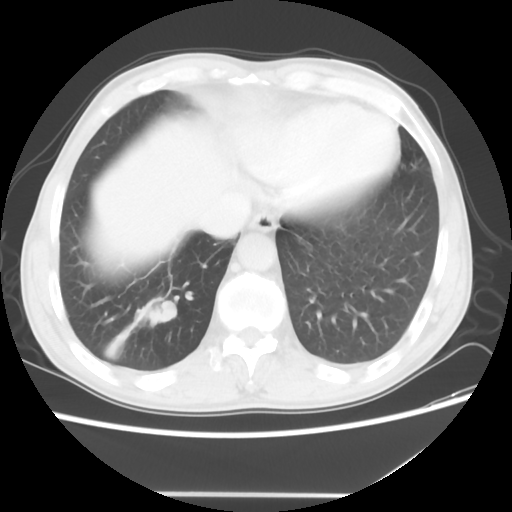
Chest CT, one axial slice; position 12 of 56 along the scan axis; 120 kVp; lung window (W 1500 / L -600 HU); 5 mm slice thickness; 512 × 512 image matrix, field of view 344 × 344 mm. Male patient, age 65 years. From the clinical record (not read from this slice): clinical TNM (as recorded): T1c N3 M0.
Structures marked on this image (rectangle marked by the reading radiologist):
- lung tumour (recorded histology: small cell carcinoma): bounding box (x1, y1, x2, y2) in pixels: (137, 295, 187, 327)